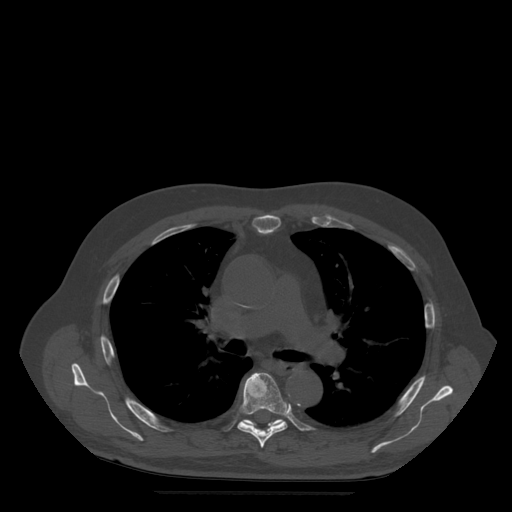
CT including the spine, one axial slice. Slice 350 of 522 in the series (ordered by position). Bone window (W 1800 / L 400 HU). 512 × 512 image matrix, field of view 420 × 420 mm. Patient age 72 years. From the clinical record (not read from this slice): primary cancer: prostate.
Outlined on this slice (semi-automatically segmented with operator editing):
- T6 vertebra: box from (x=238, y=373) to (x=290, y=448) px
- T7 vertebra: (x=244, y=419)–(x=284, y=429)